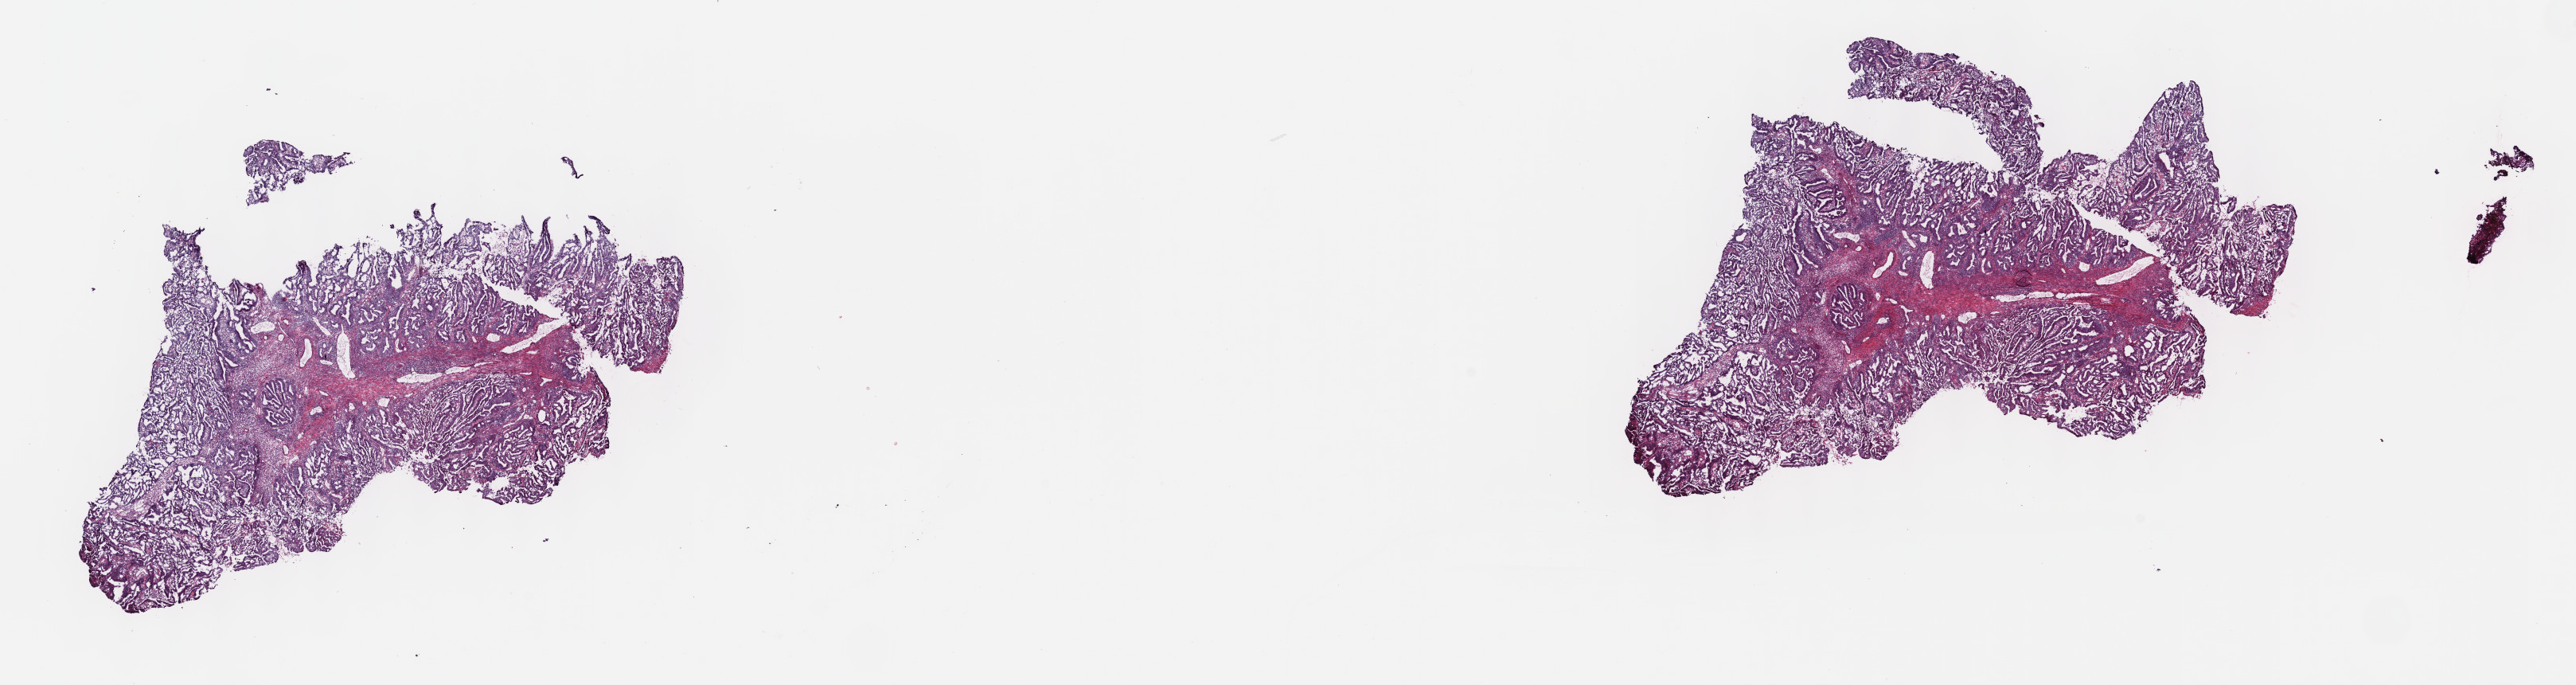
Digitized H&E tissue section (whole slide) — whole scanned area (about 26.2 x 7.0 mm) shown as a low-resolution overview; frozen section from the top of the tissue portion; primary tumour sample from the cervix. Female patient; age at initial diagnosis 44 years. Histologic grade: G1 (well differentiated). Pathologist review of this section (percent, as recorded): tumour cells 100%, tumour nuclei 65%, normal cells 0%, stromal cells 0%, necrosis 0%. Inflammatory infiltration, as recorded: lymphocyte infiltration 3%, monocyte infiltration 0%, neutrophil infiltration 0%.
* FIGO stage: IB1
* lymph nodes positive (case pathology): 0 of 47 examined
* pathologic diagnosis: Endometrioid adenocarcinoma, NOS